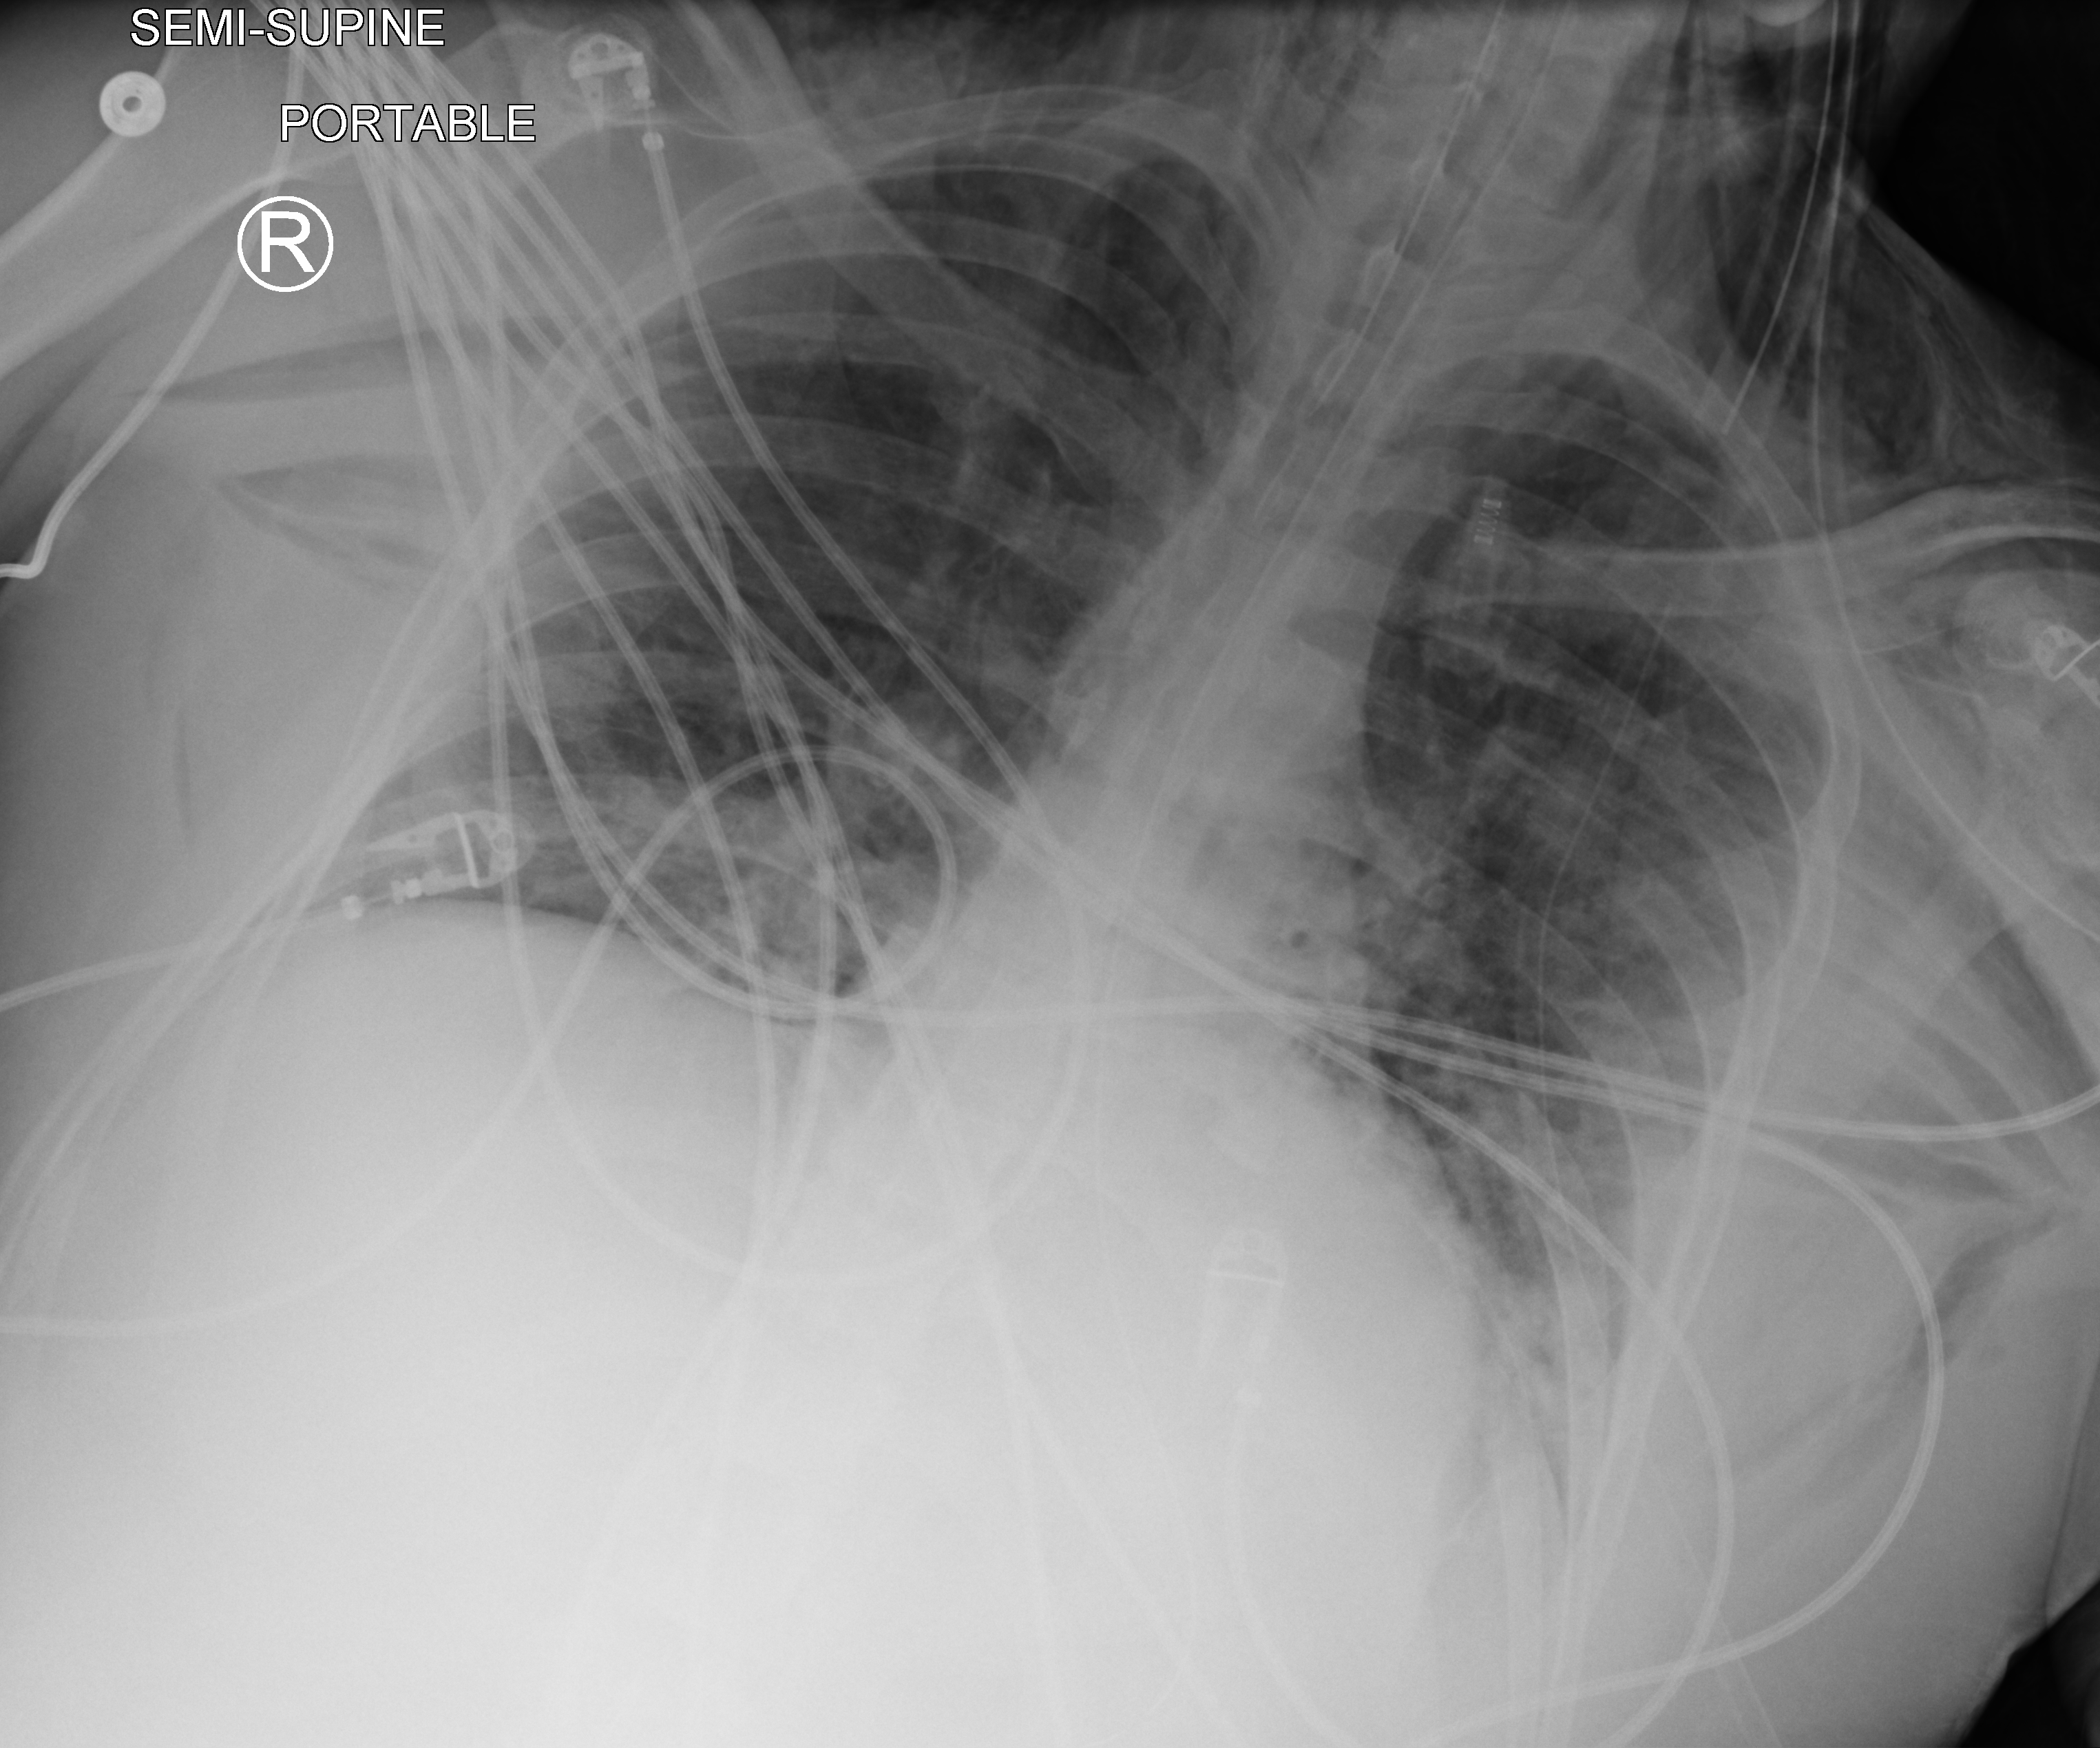
Portable chest radiograph, anteroposterior (AP) projection. Patient hospitalised with COVID-19; male, aged 18–59 years.
Admission-level facts for this patient (not findings on this image; timing relative to this image not recorded): length of hospital stay: 22 days.